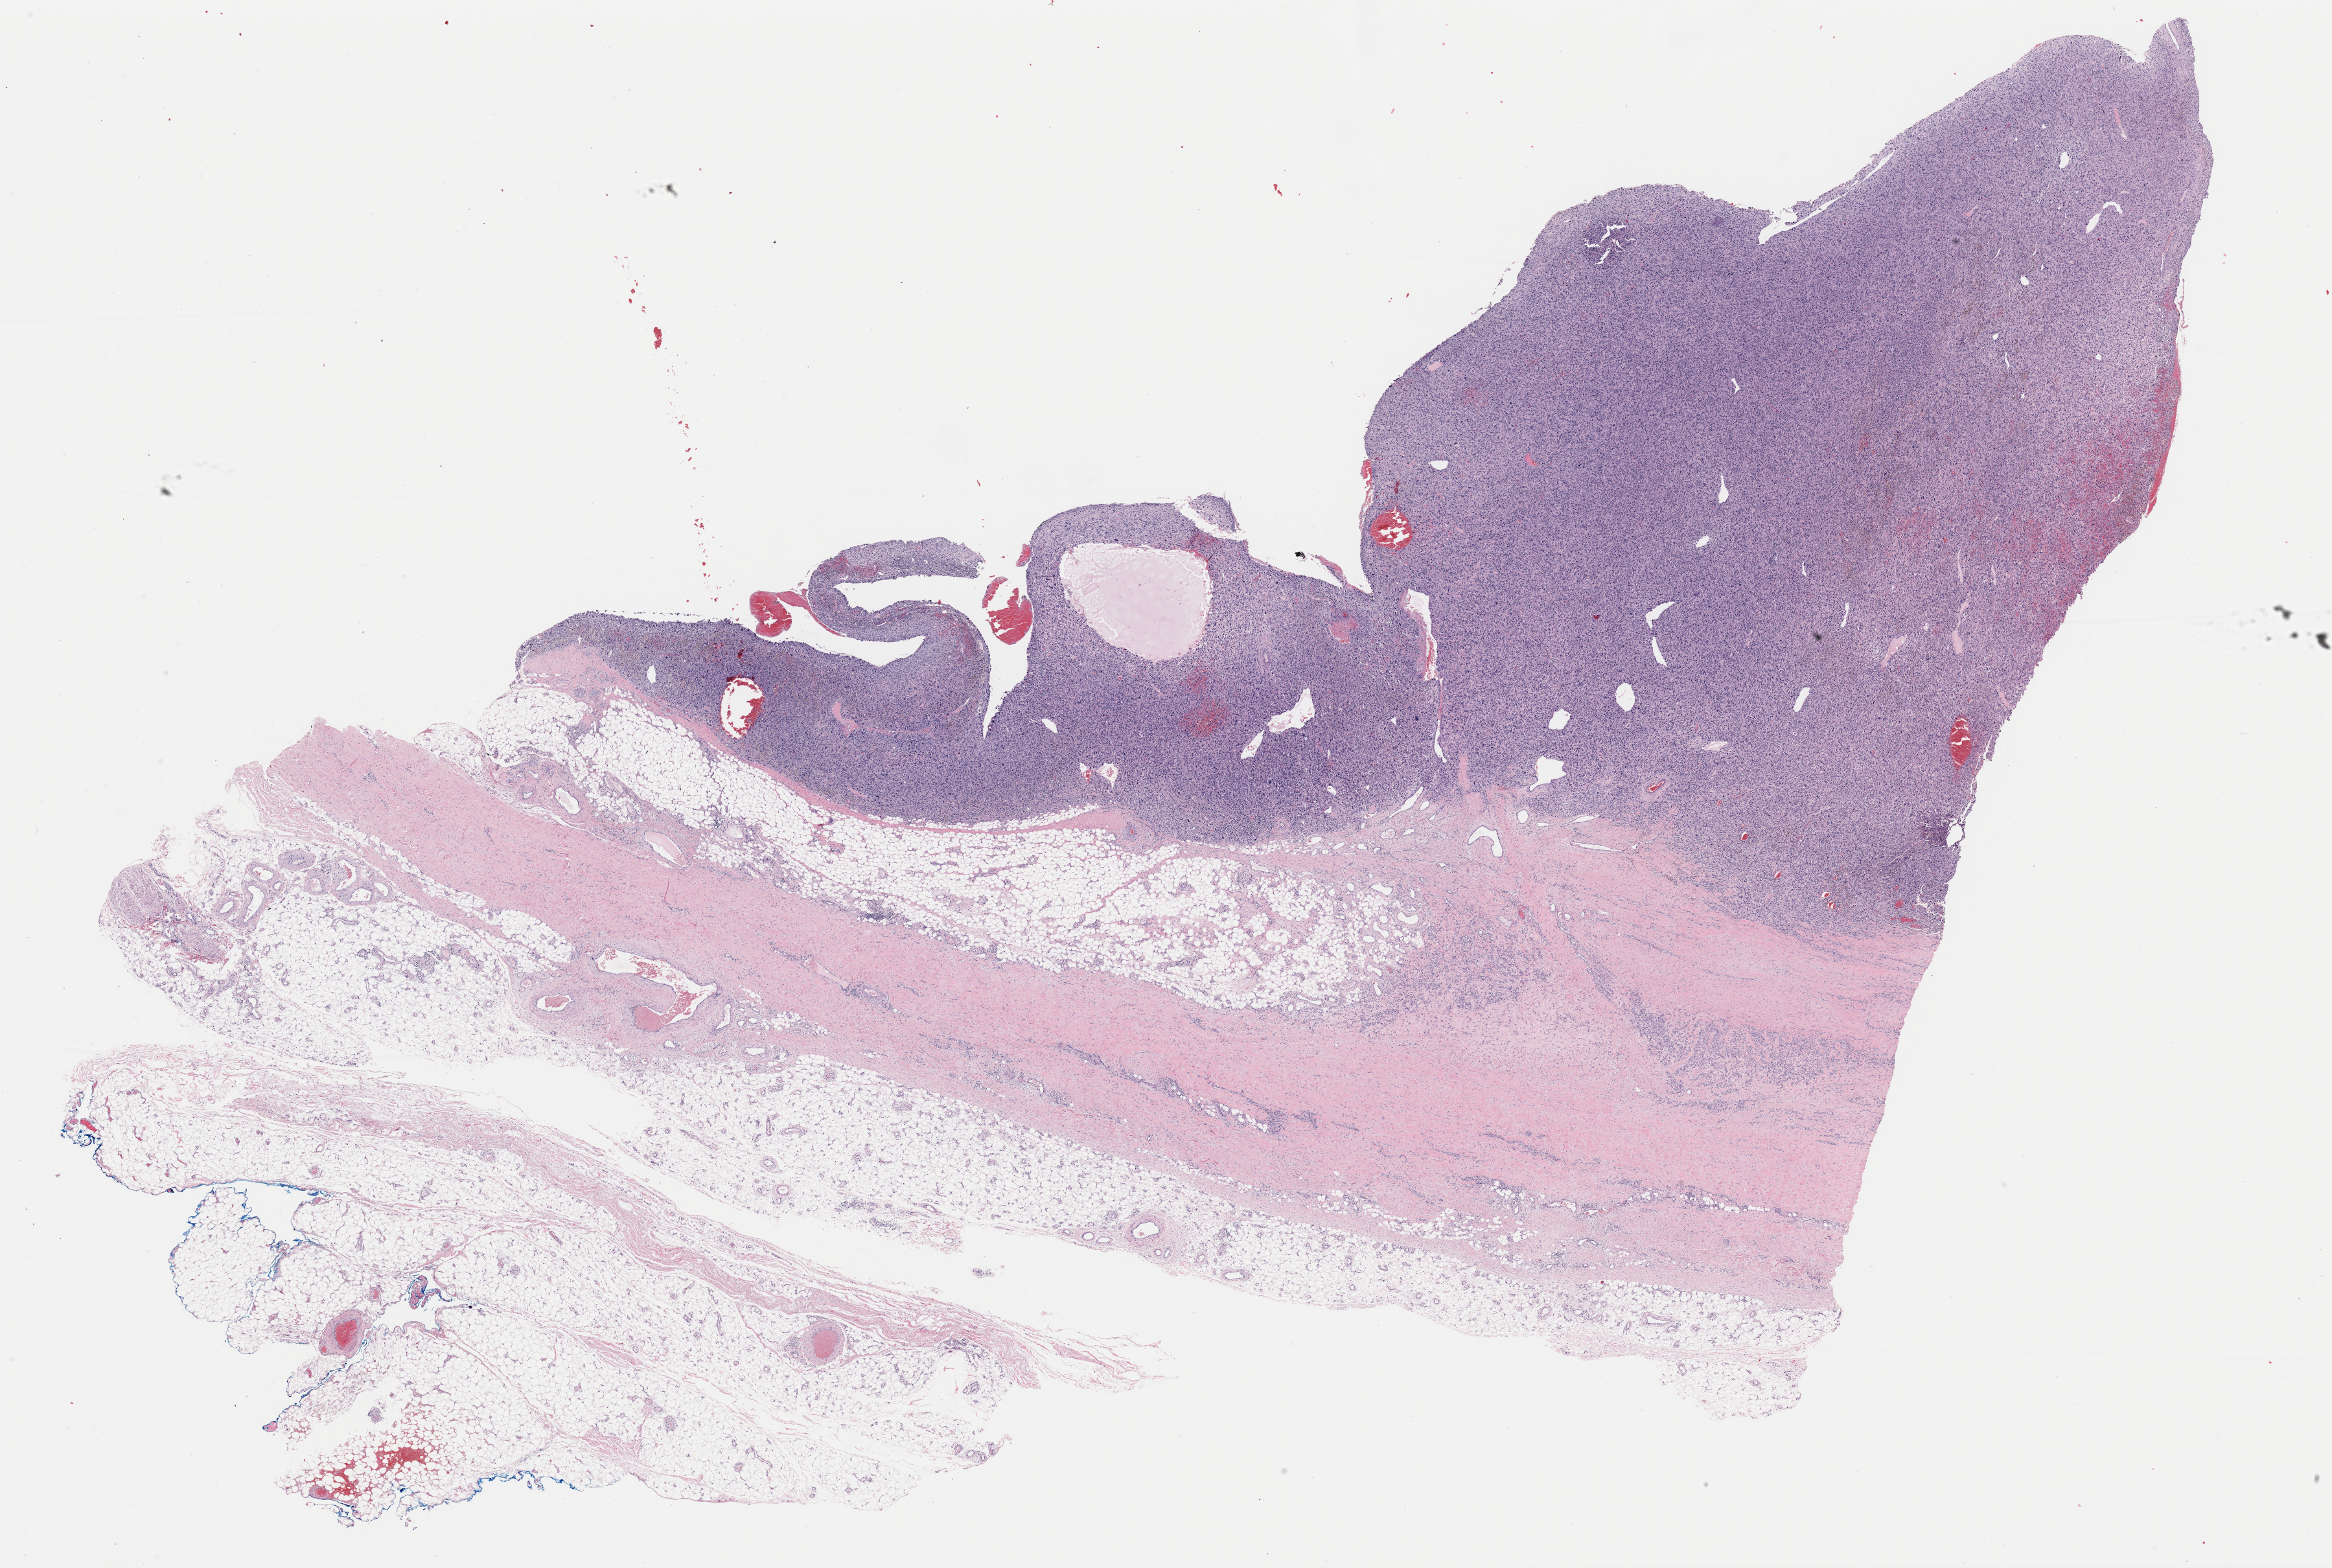
H&E whole-slide image — whole scanned area (about 28.4 x 19.1 mm, from a 40x scan) shown as a low-resolution overview, FFPE section, sample: primary tumour, connective, subcutaneous and other soft tissues. Female, age 75 years at initial diagnosis.
Histologic diagnosis: Malignant fibrous histiocytoma (connective, subcutaneous and other soft tissues of lower limb and hip).